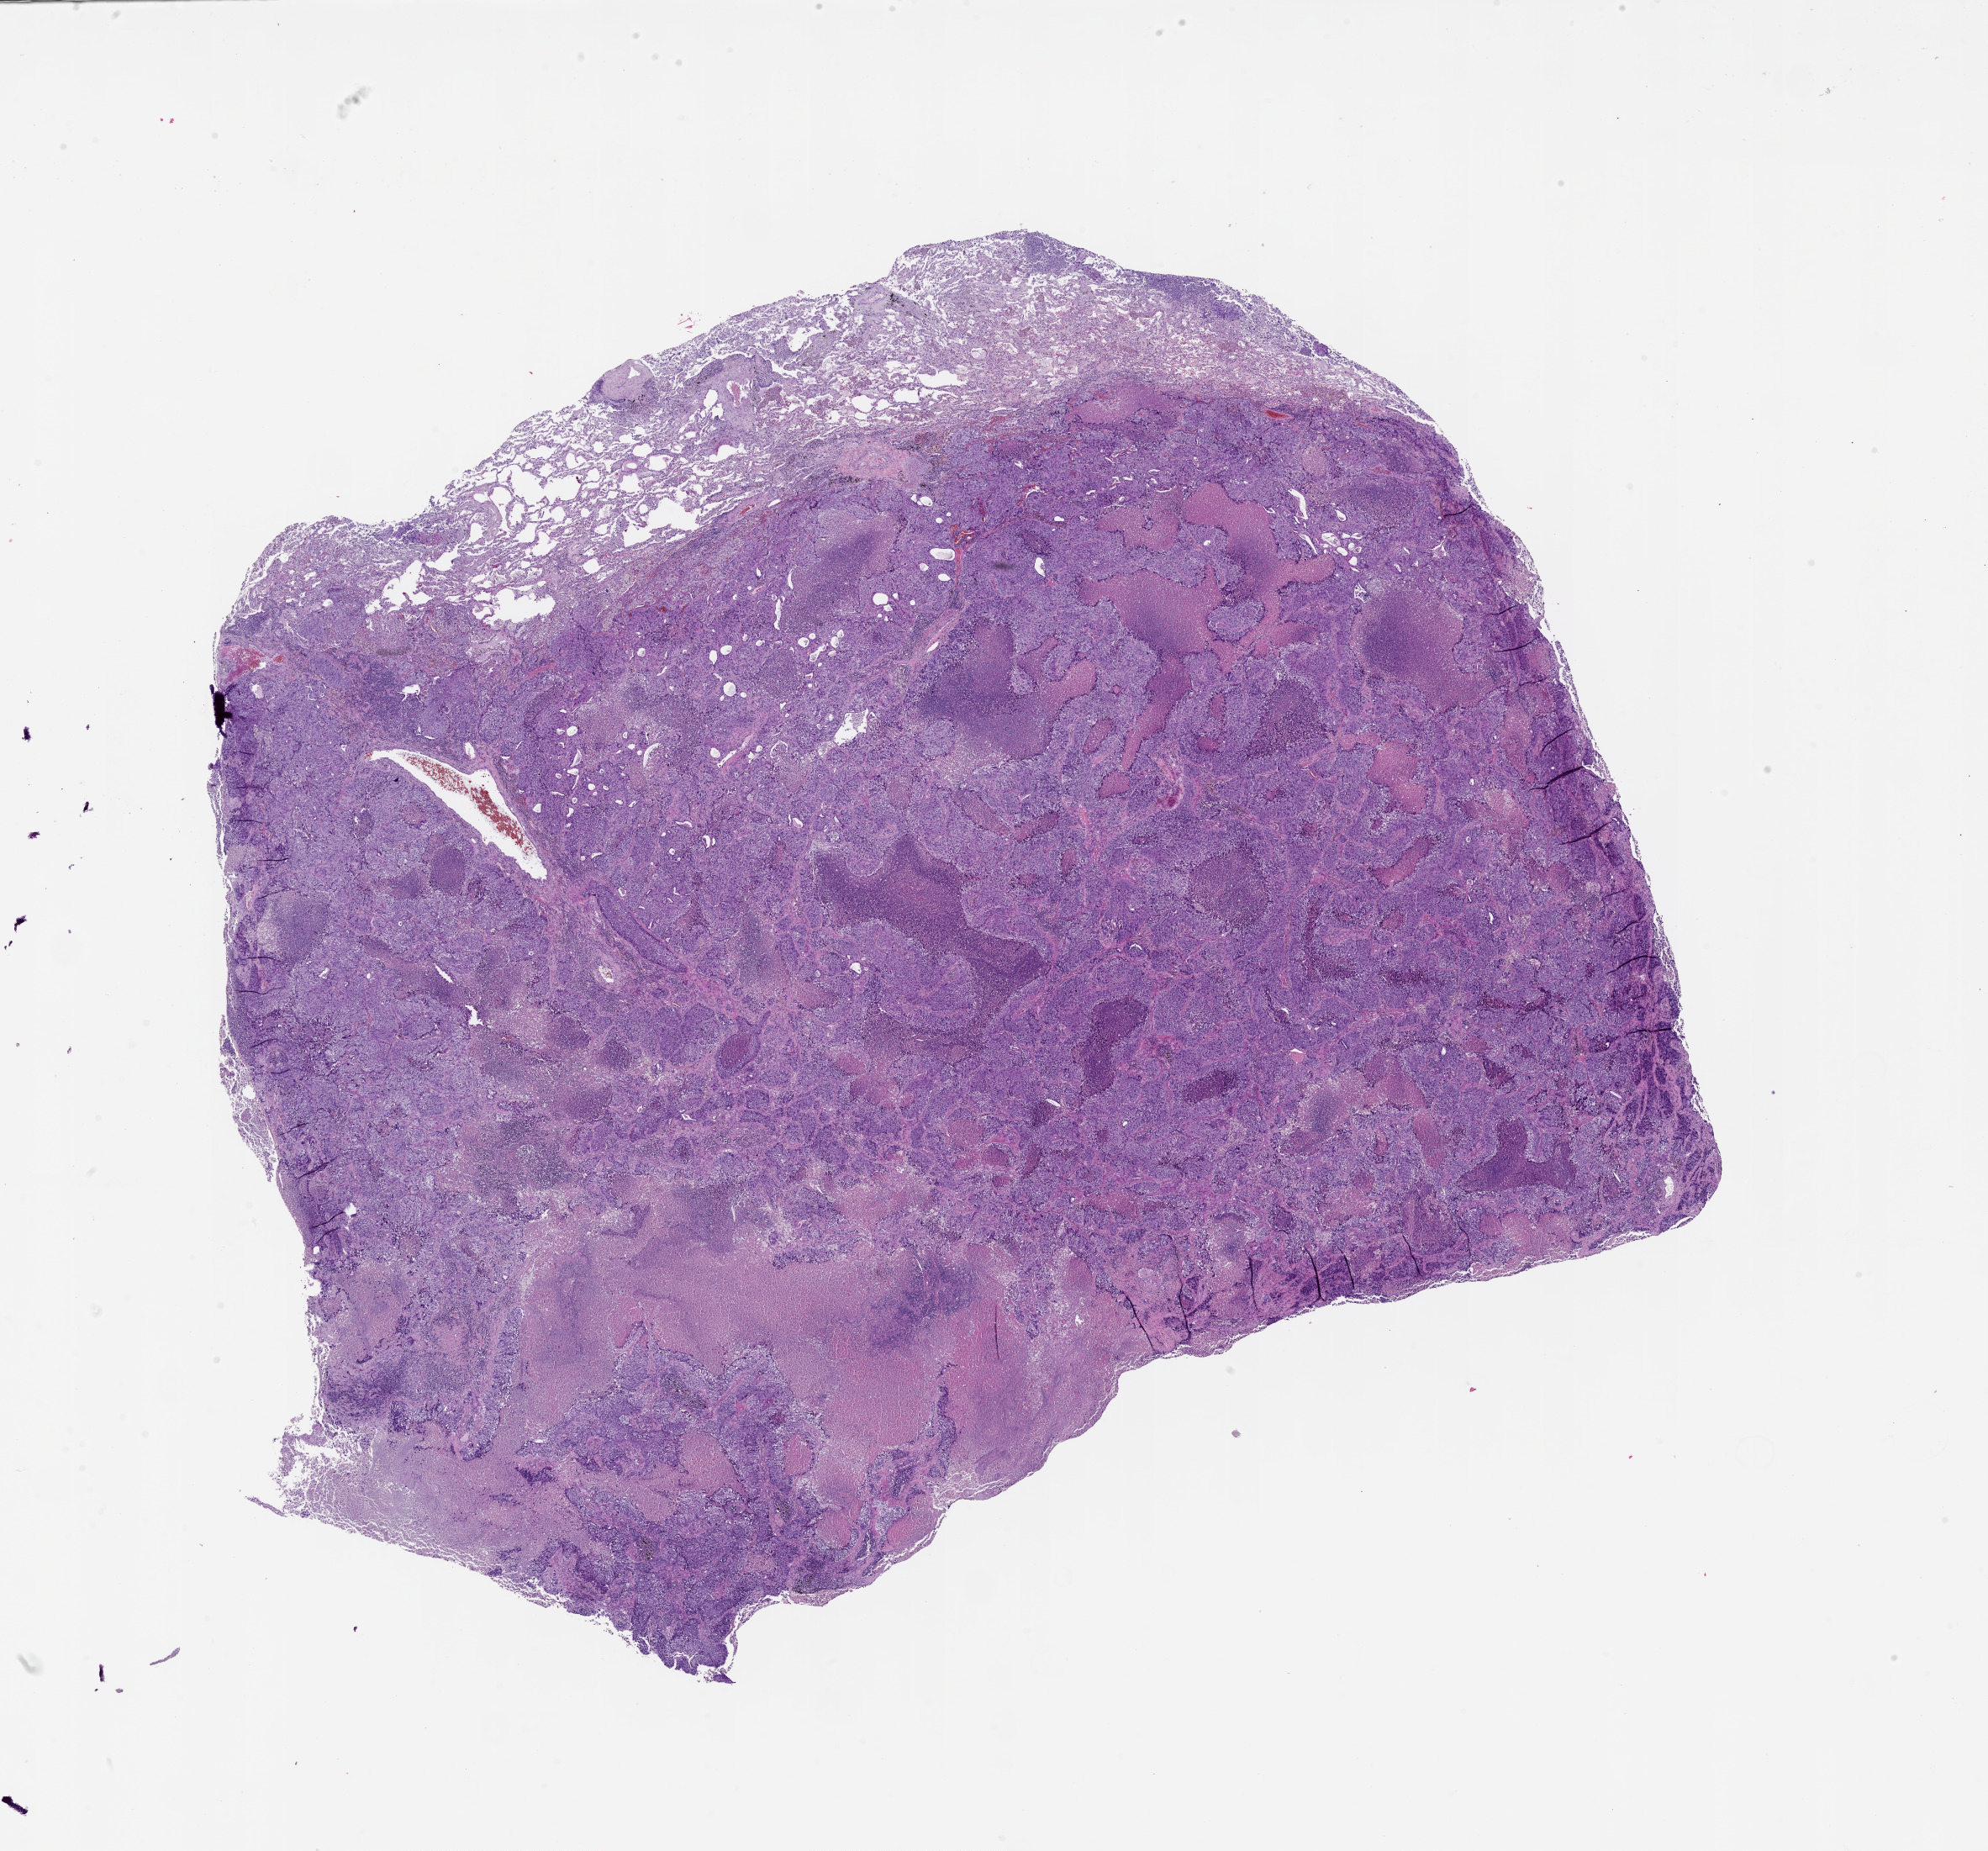
H&E whole-slide image, a low-resolution overview of the entire scanned area, about 19.0 x 17.7 mm; tumour tissue sample, lung. 54-year-old male patient.
• patient diagnosis (cohort enrolment): squamous cell carcinoma (lung)